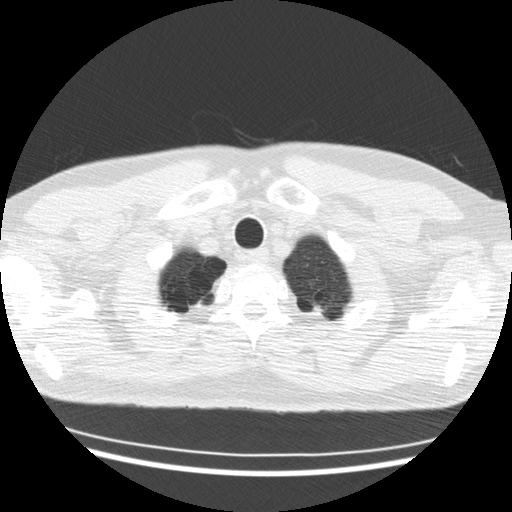
Low-dose screening chest CT, one axial slice; position 160 of 176 along the scan axis; reconstruction kernel STANDARD; 120 kVp; lung window (W 1500 / L -600 HU); 2.5 mm slice thickness; 512 × 512 image matrix.
Annotated regions visible in this slice (outlined manually by an expert reader):
- lesion 1 (tumor, upper lobe of left lung): bounding box (x1, y1, x2, y2) in pixels: (312, 306, 326, 312)